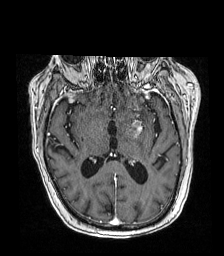
Brain MRI from a brain-tumour surgery series, one axial slice; slice 90 of 192 in the series (ordered by position); T1-weighted post-contrast; 1 mm slice thickness; 224 × 256 image matrix, field of view 219 × 250 mm. Case-level facts recorded for this patient, not image findings: histopathology: Metastatic carcinoma from lung primary.
Structures marked on this image (outlined manually by an expert reader):
- tumour: bounding box (x1, y1, x2, y2) in pixels: (126, 116, 139, 135)